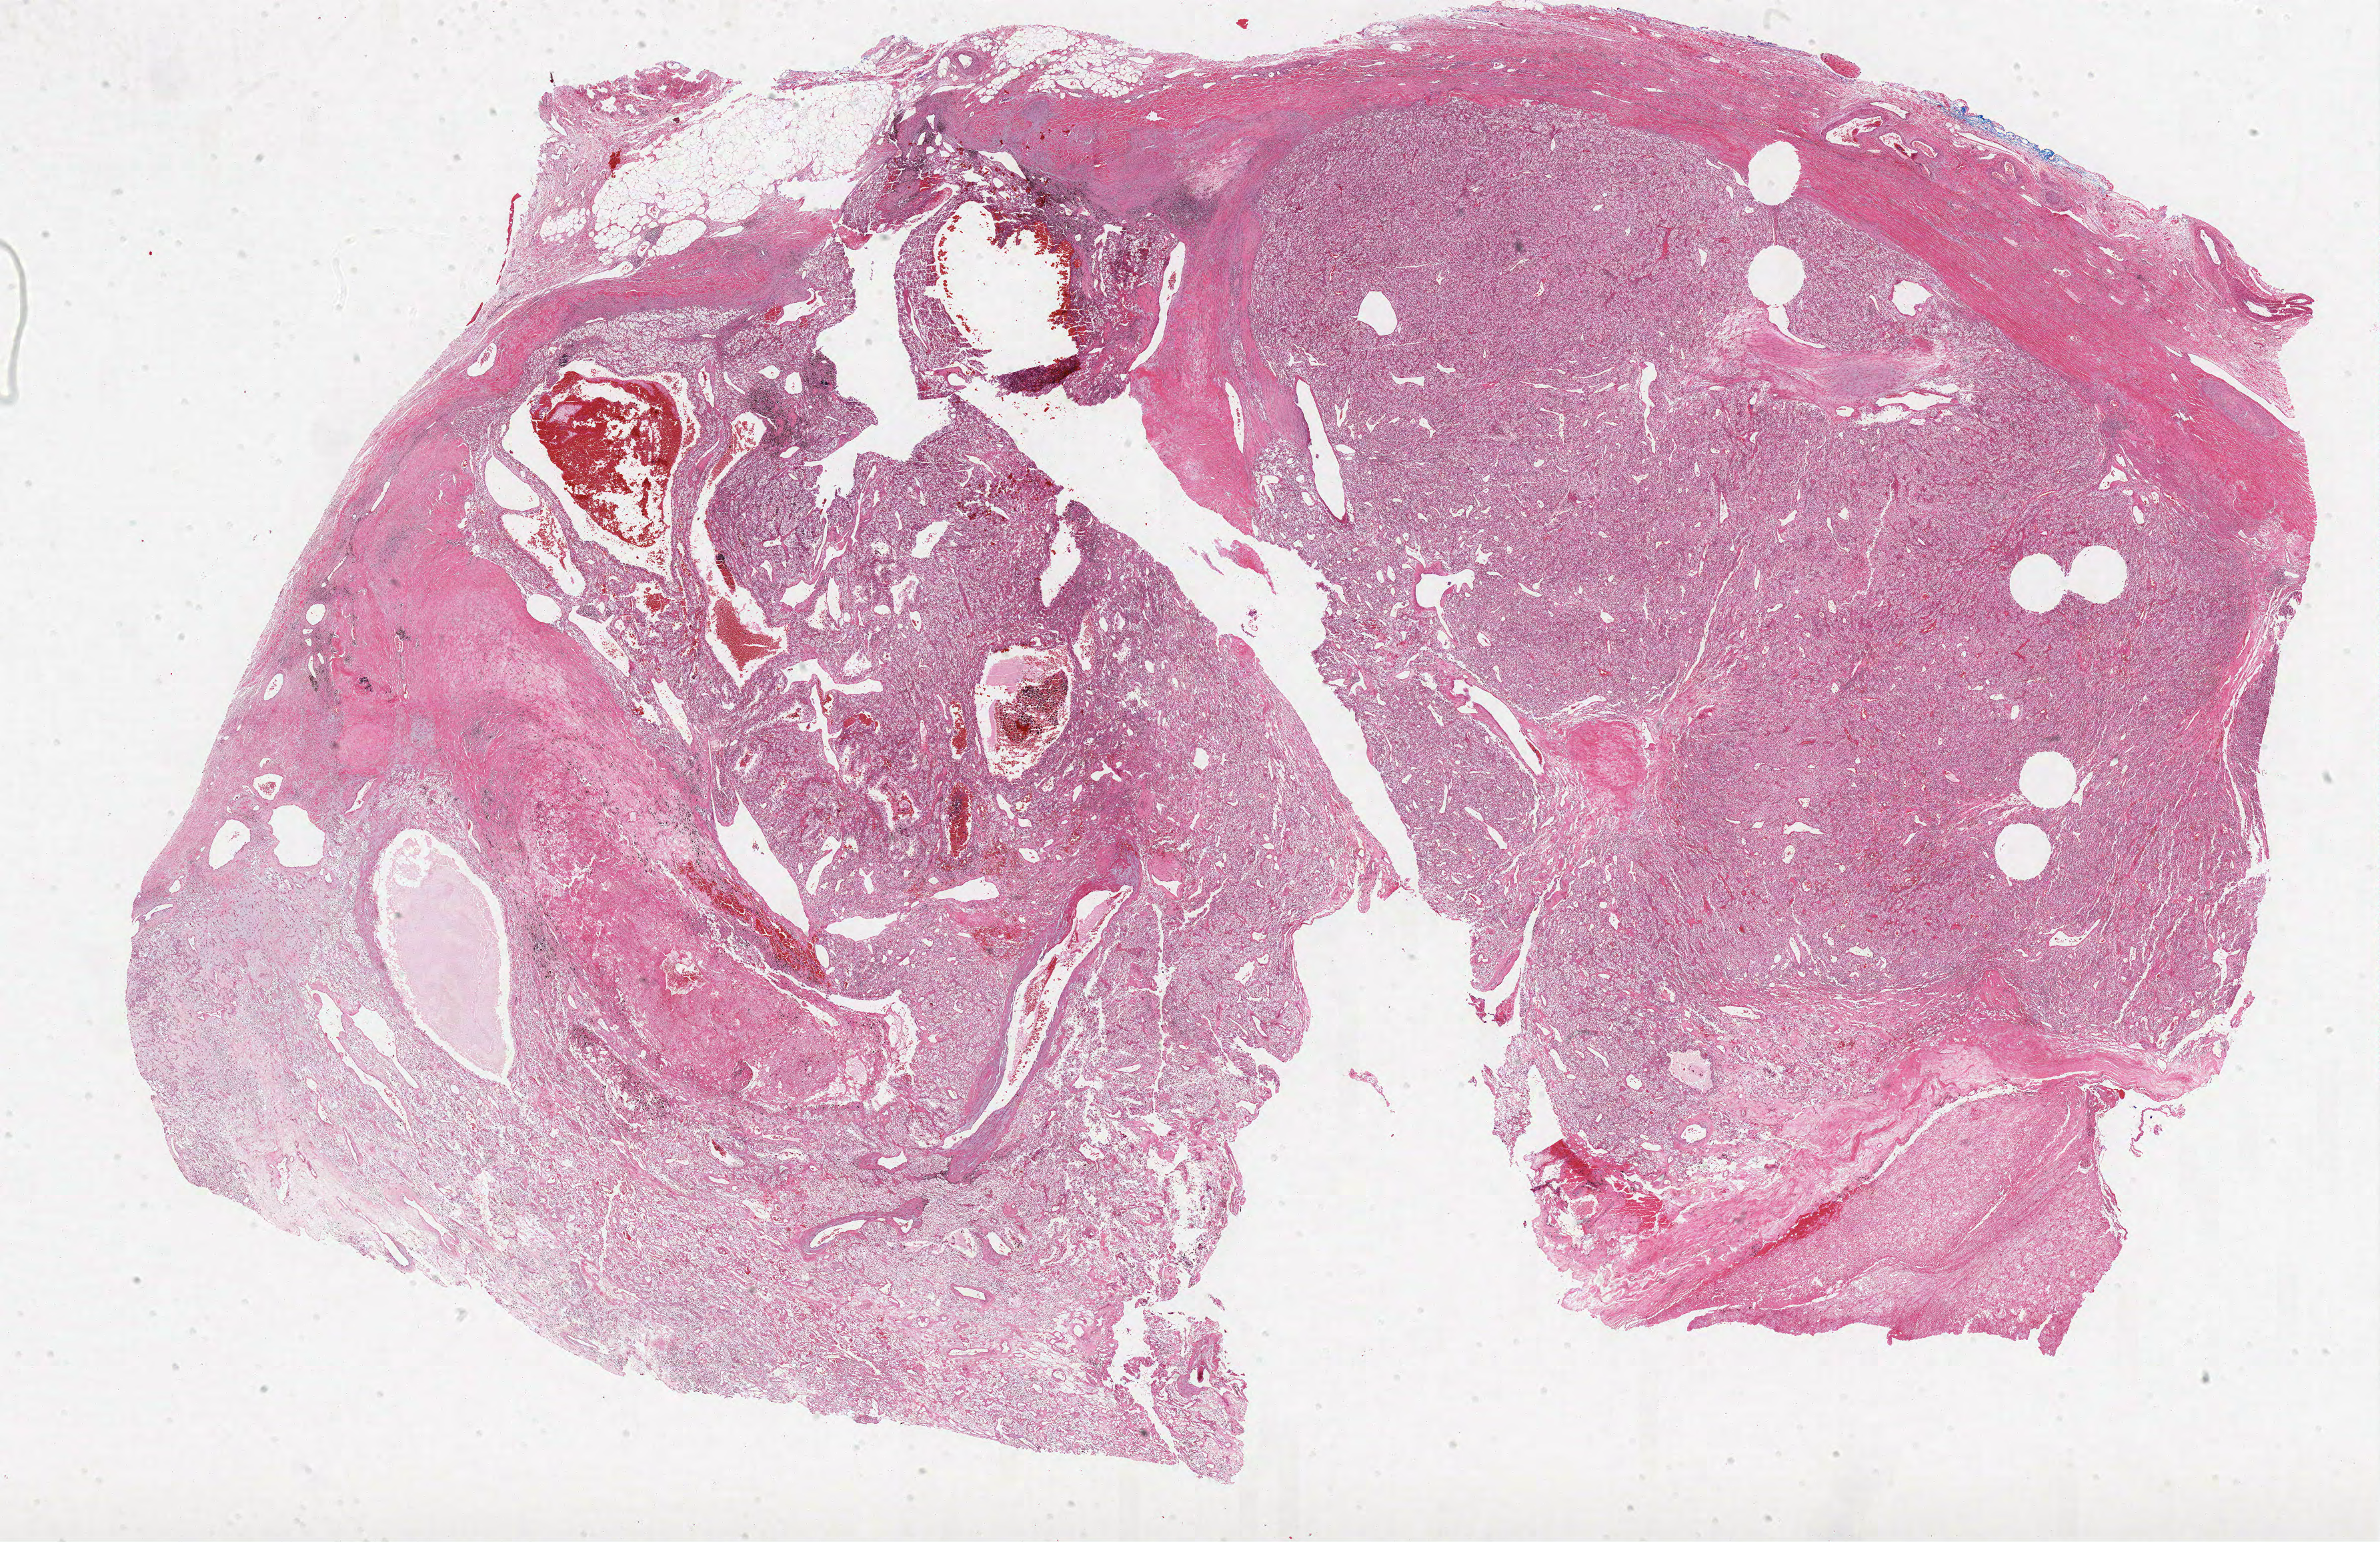
Hematoxylin and eosin (H&E) stained whole-slide image — low-resolution overview of the scanned area, about 28.5 x 18.5 mm, formalin-fixed paraffin-embedded (FFPE) diagnostic section, kidney, primary tumour sample. Male patient; age at initial diagnosis 47 years.
Diagnosis: Clear cell adenocarcinoma, NOS.